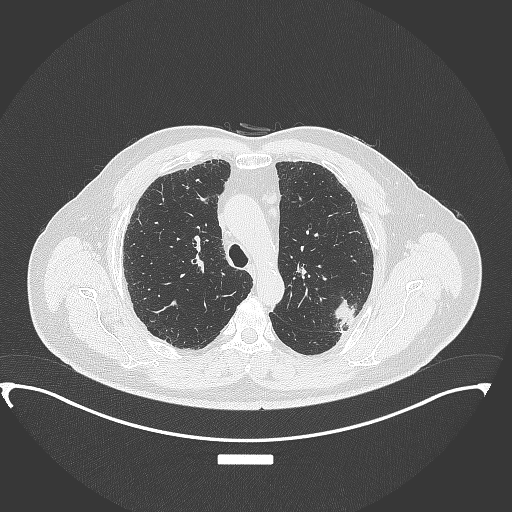
Chest CT, one axial slice. Position 258 of 350 along the scan axis. Reconstruction kernel B70f. Lung window (W 1500 / L -600 HU). 1 mm slice thickness. 512 × 512 image matrix, field of view 459 × 459 mm. Male patient, age 64 years. Case-level facts recorded for this patient, not image findings: clinical TNM (as recorded): T1c N1 M1.
Structures marked on this image (rectangle marked by the reading radiologist):
- lung tumour (recorded histology: adenocarcinoma): bounding box [x1, y1, x2, y2] px = [334, 296, 358, 338]